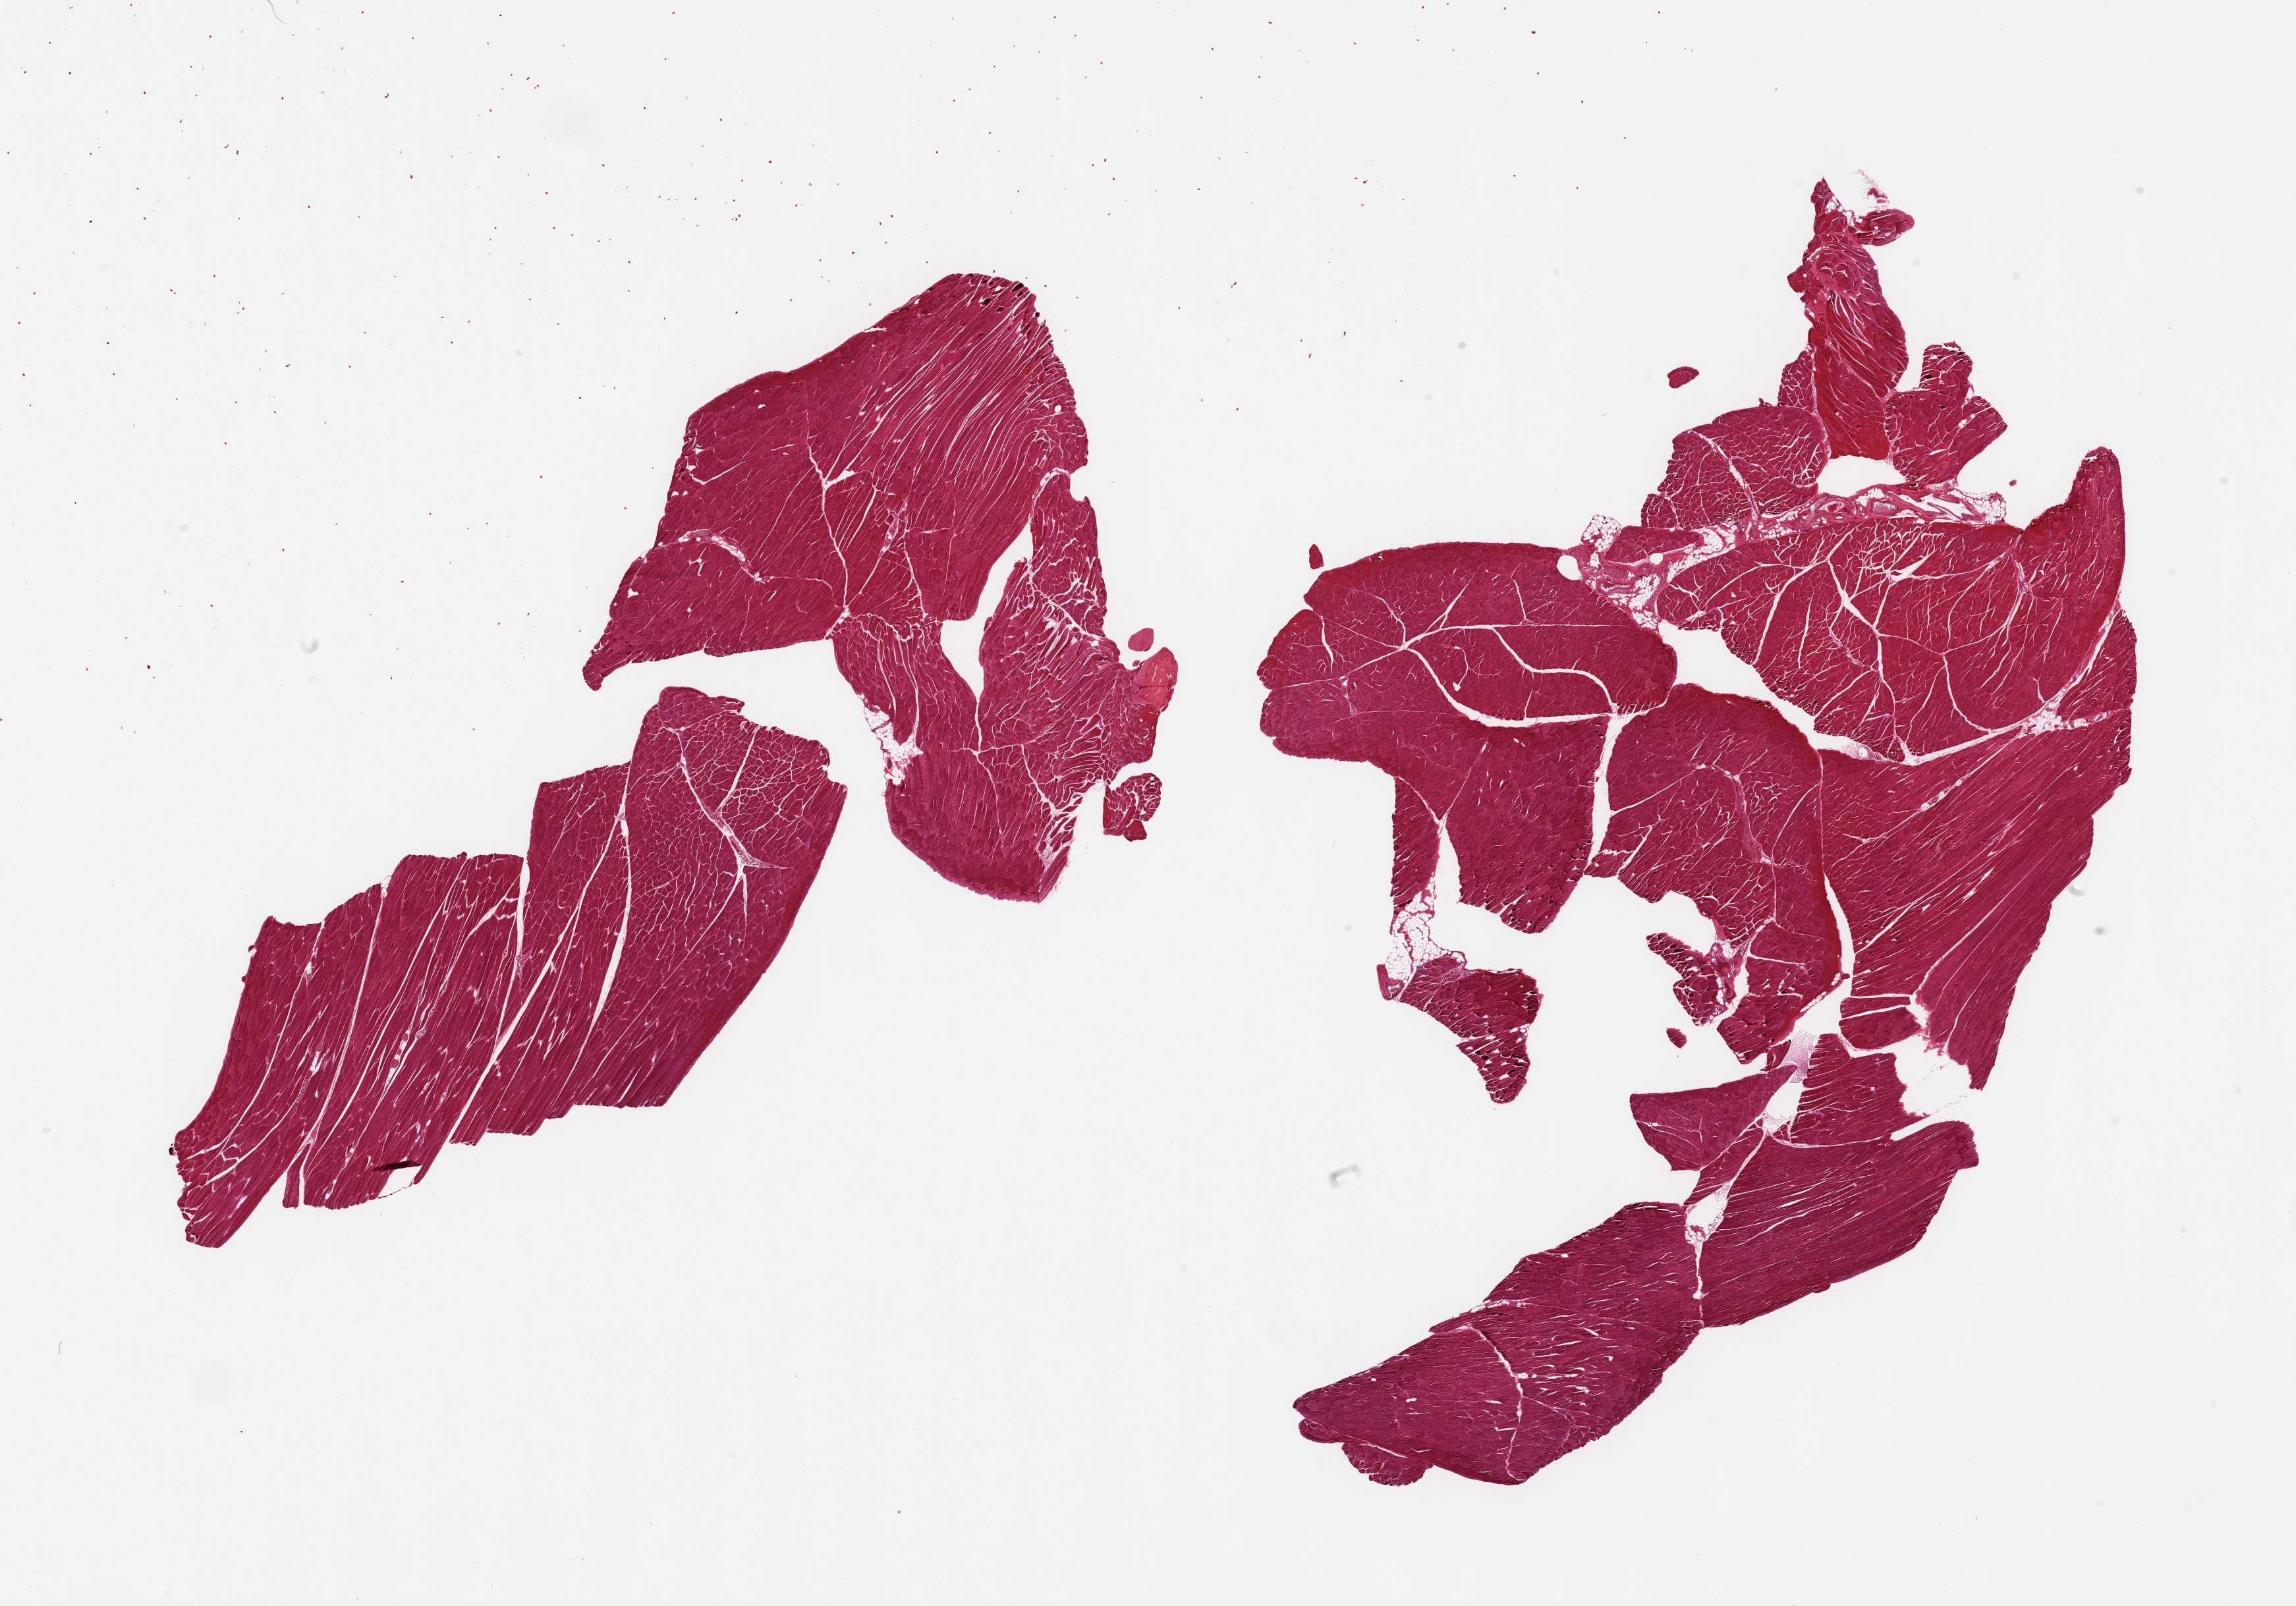
H&E whole-slide image, brightfield, whole scanned area (about 27.6 x 19.3 mm, from a 20x scan) shown as a low-resolution overview, PAXgene-fixed paraffin-embedded (PFPE) section, sampled site (target tissue): skeletal muscle, donor tissue sample. Donor: male.
• review note (as recorded): 2 fragmented pieces; striations visible; minimal fat content